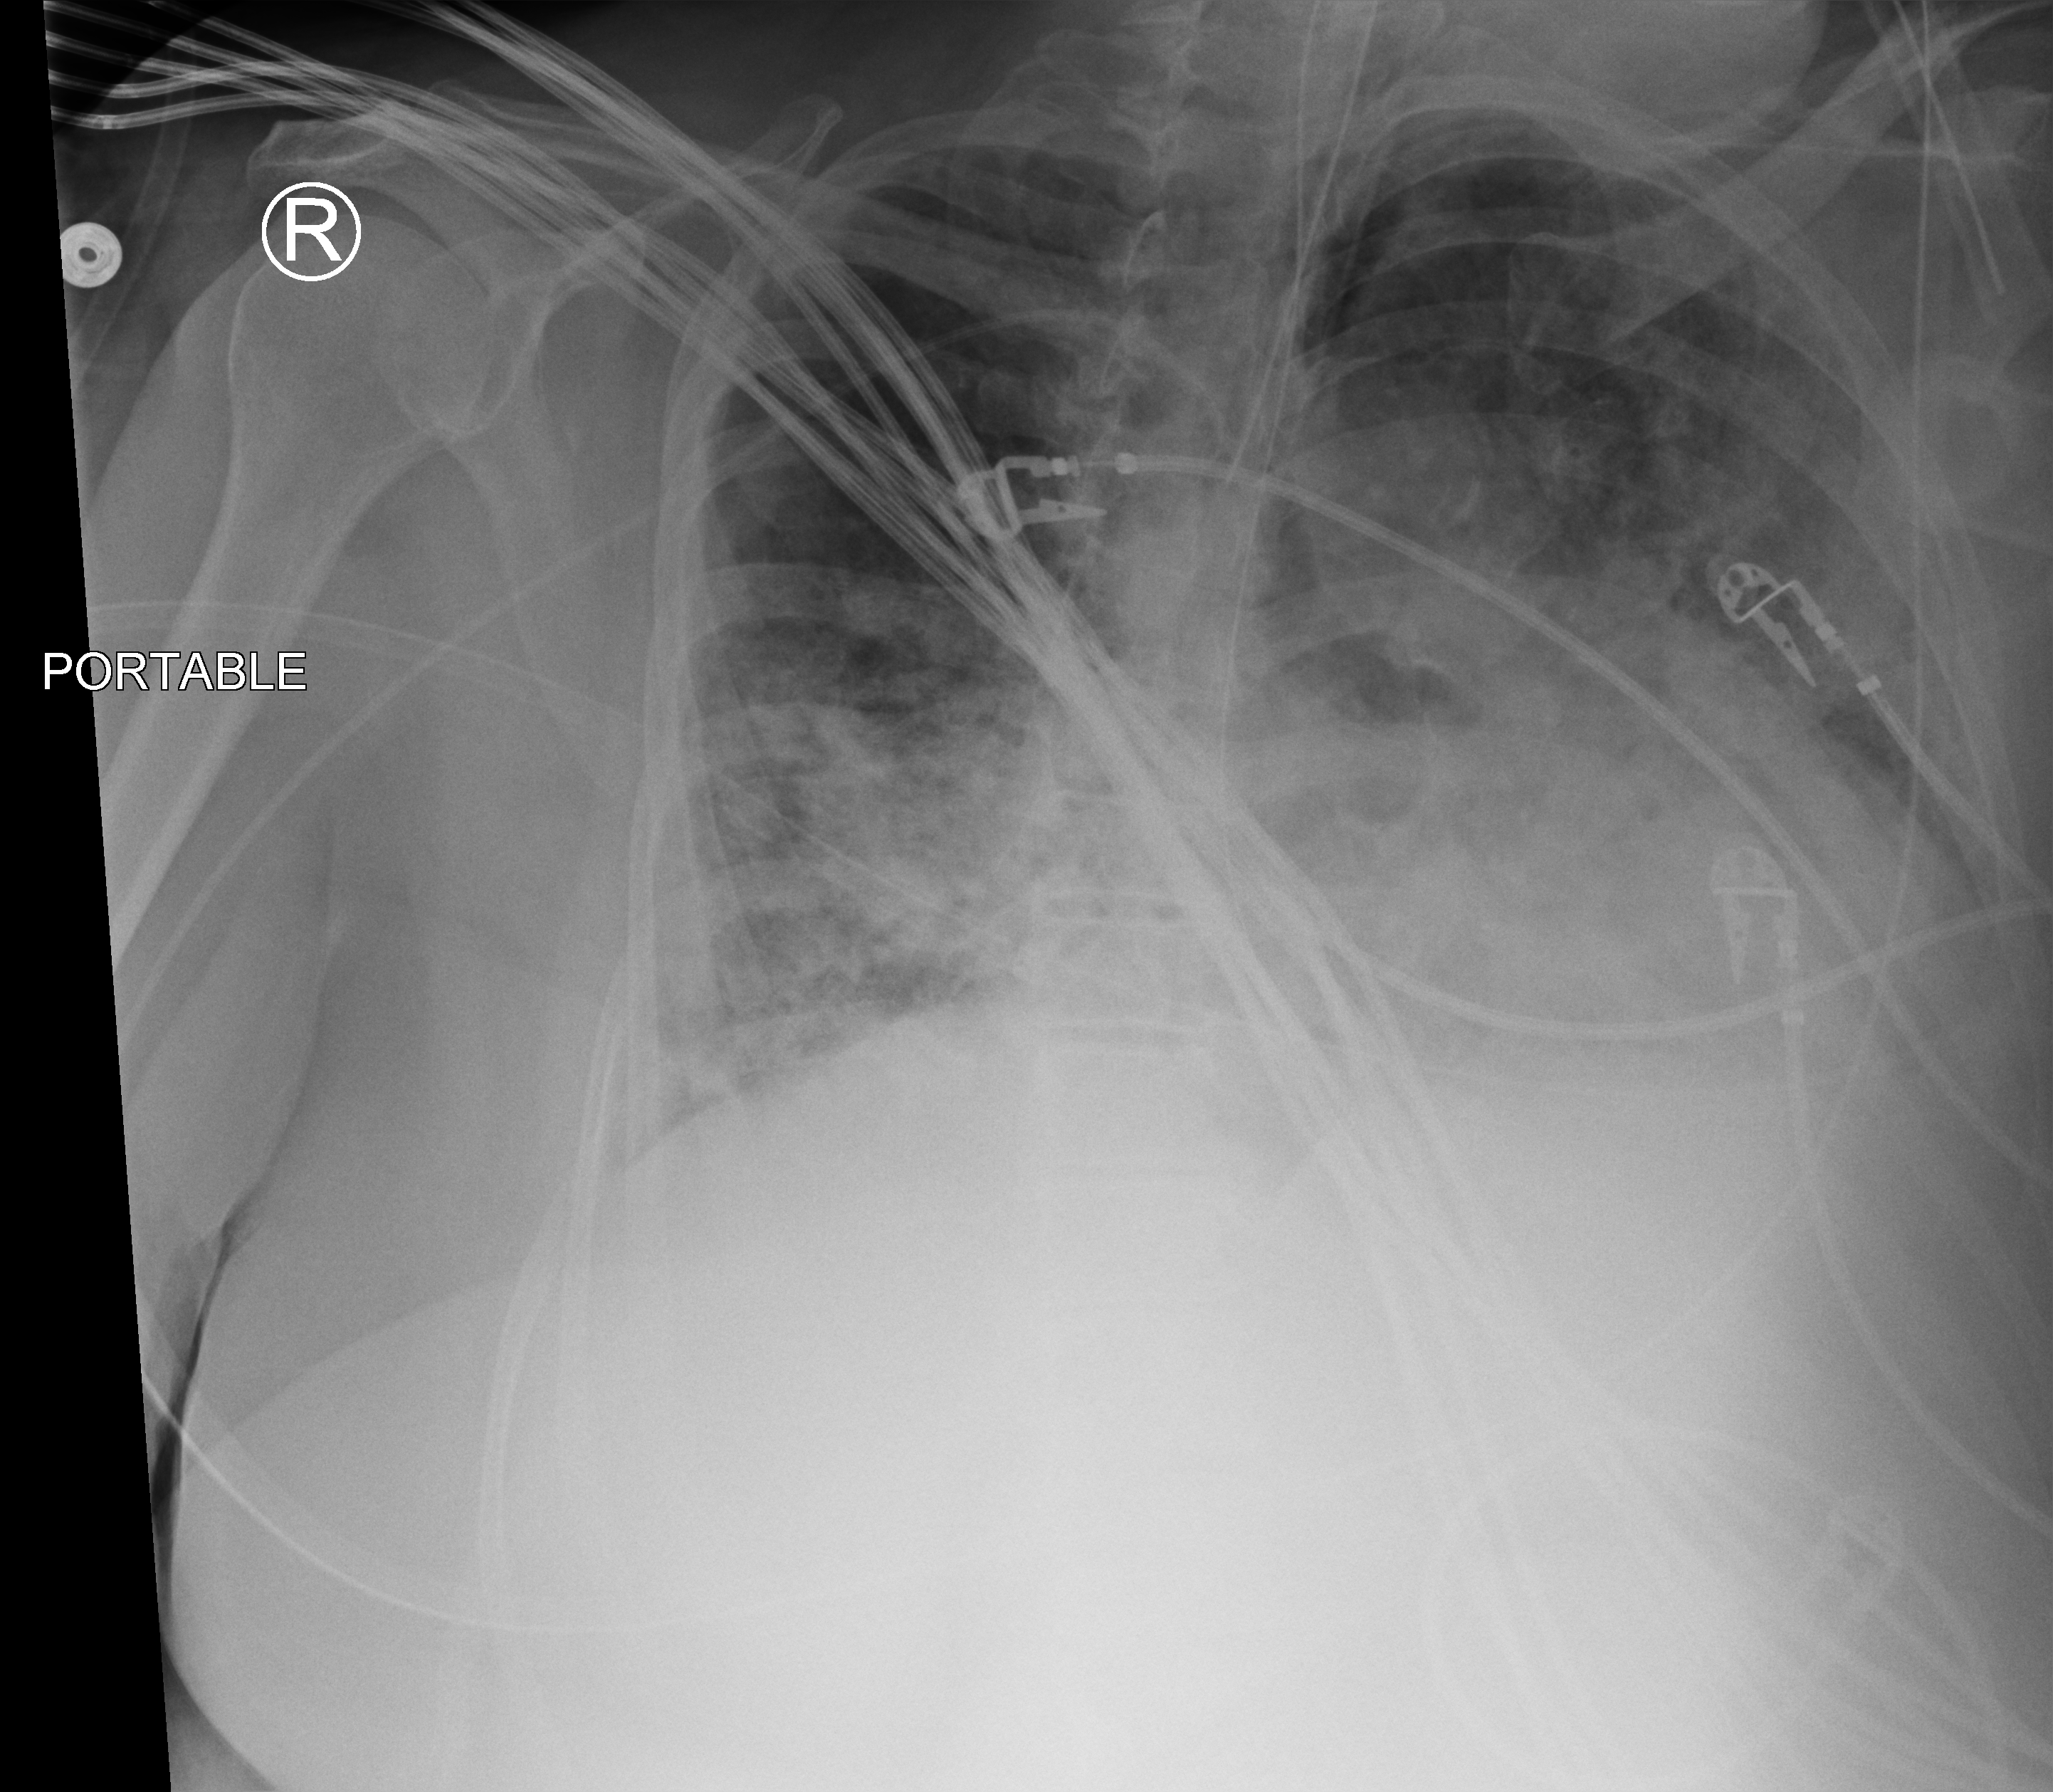
Portable chest radiograph, anteroposterior (AP) projection. Patient hospitalised with COVID-19; female, aged 60–74 years.
Admission-level facts for this patient (not findings on this image; timing relative to this image not recorded): mechanically ventilated during this hospital stay: yes.